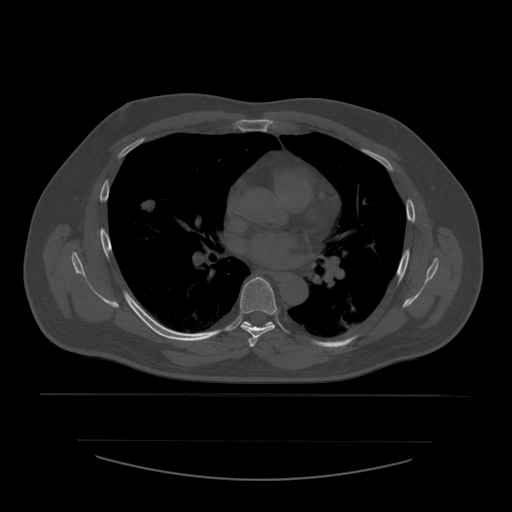
CT including the spine, one axial slice. Slice 375 of 532 in the series (ordered by position). 120 kVp. Bone window (W 1800 / L 400 HU). 1.25 mm slice thickness. 512 × 512 image matrix, field of view 441 × 441 mm. Patient age 44 years. Case-level facts recorded for this patient, not image findings: primary cancer: soft tissue sarcoma.
Outlined on this slice (semi-automatic segmentation, software-assisted and operator-edited):
- T5 vertebra: bounding box <249,337,258,347> (left, top, right, bottom; pixels)
- T6 vertebra: <240,277,278,339>
- T7 vertebra: <244,322,272,327>